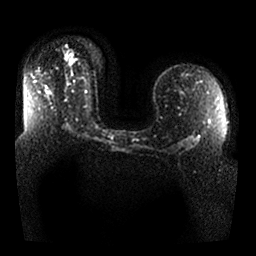
Breast MRI, one axial slice. Position 15 of 25 along the scan axis. Diffusion-weighted series; image 2 of 4 stored at this slice position (different b-values; order by instance number). 1.5 T. 4 mm slice thickness. 256 × 256 image matrix, field of view 360 × 360 mm. Female patient.
Annotated regions visible in this slice (expert manual segmentation):
- tumour on diffusion-weighted imaging: box from (x=65, y=54) to (x=74, y=64) px